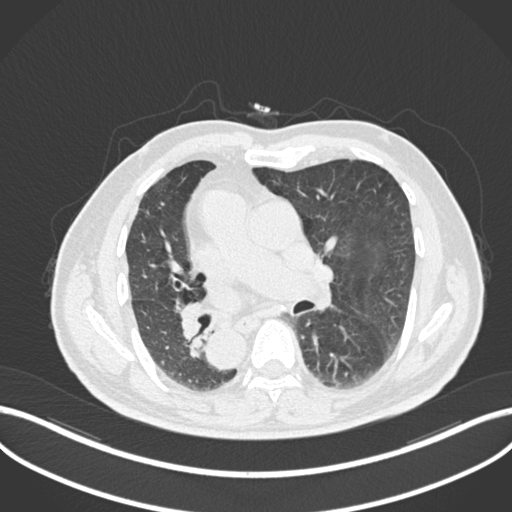
Chest CT, one axial slice. Slice 117 of 206 in the series (ordered by position). Reconstruction kernel B30f. 120 kVp. Lung window (W 1500 / L -600 HU). 512 × 512 image matrix. Male patient, age 67 years. From the clinical record (not read from this slice): clinical TNM (as recorded): T2a N0 M0.
Annotated regions visible in this slice (bounding box drawn by a radiologist):
- lung tumour (recorded histology: squamous cell carcinoma): bounding box <176,295,211,341> (left, top, right, bottom; pixels)